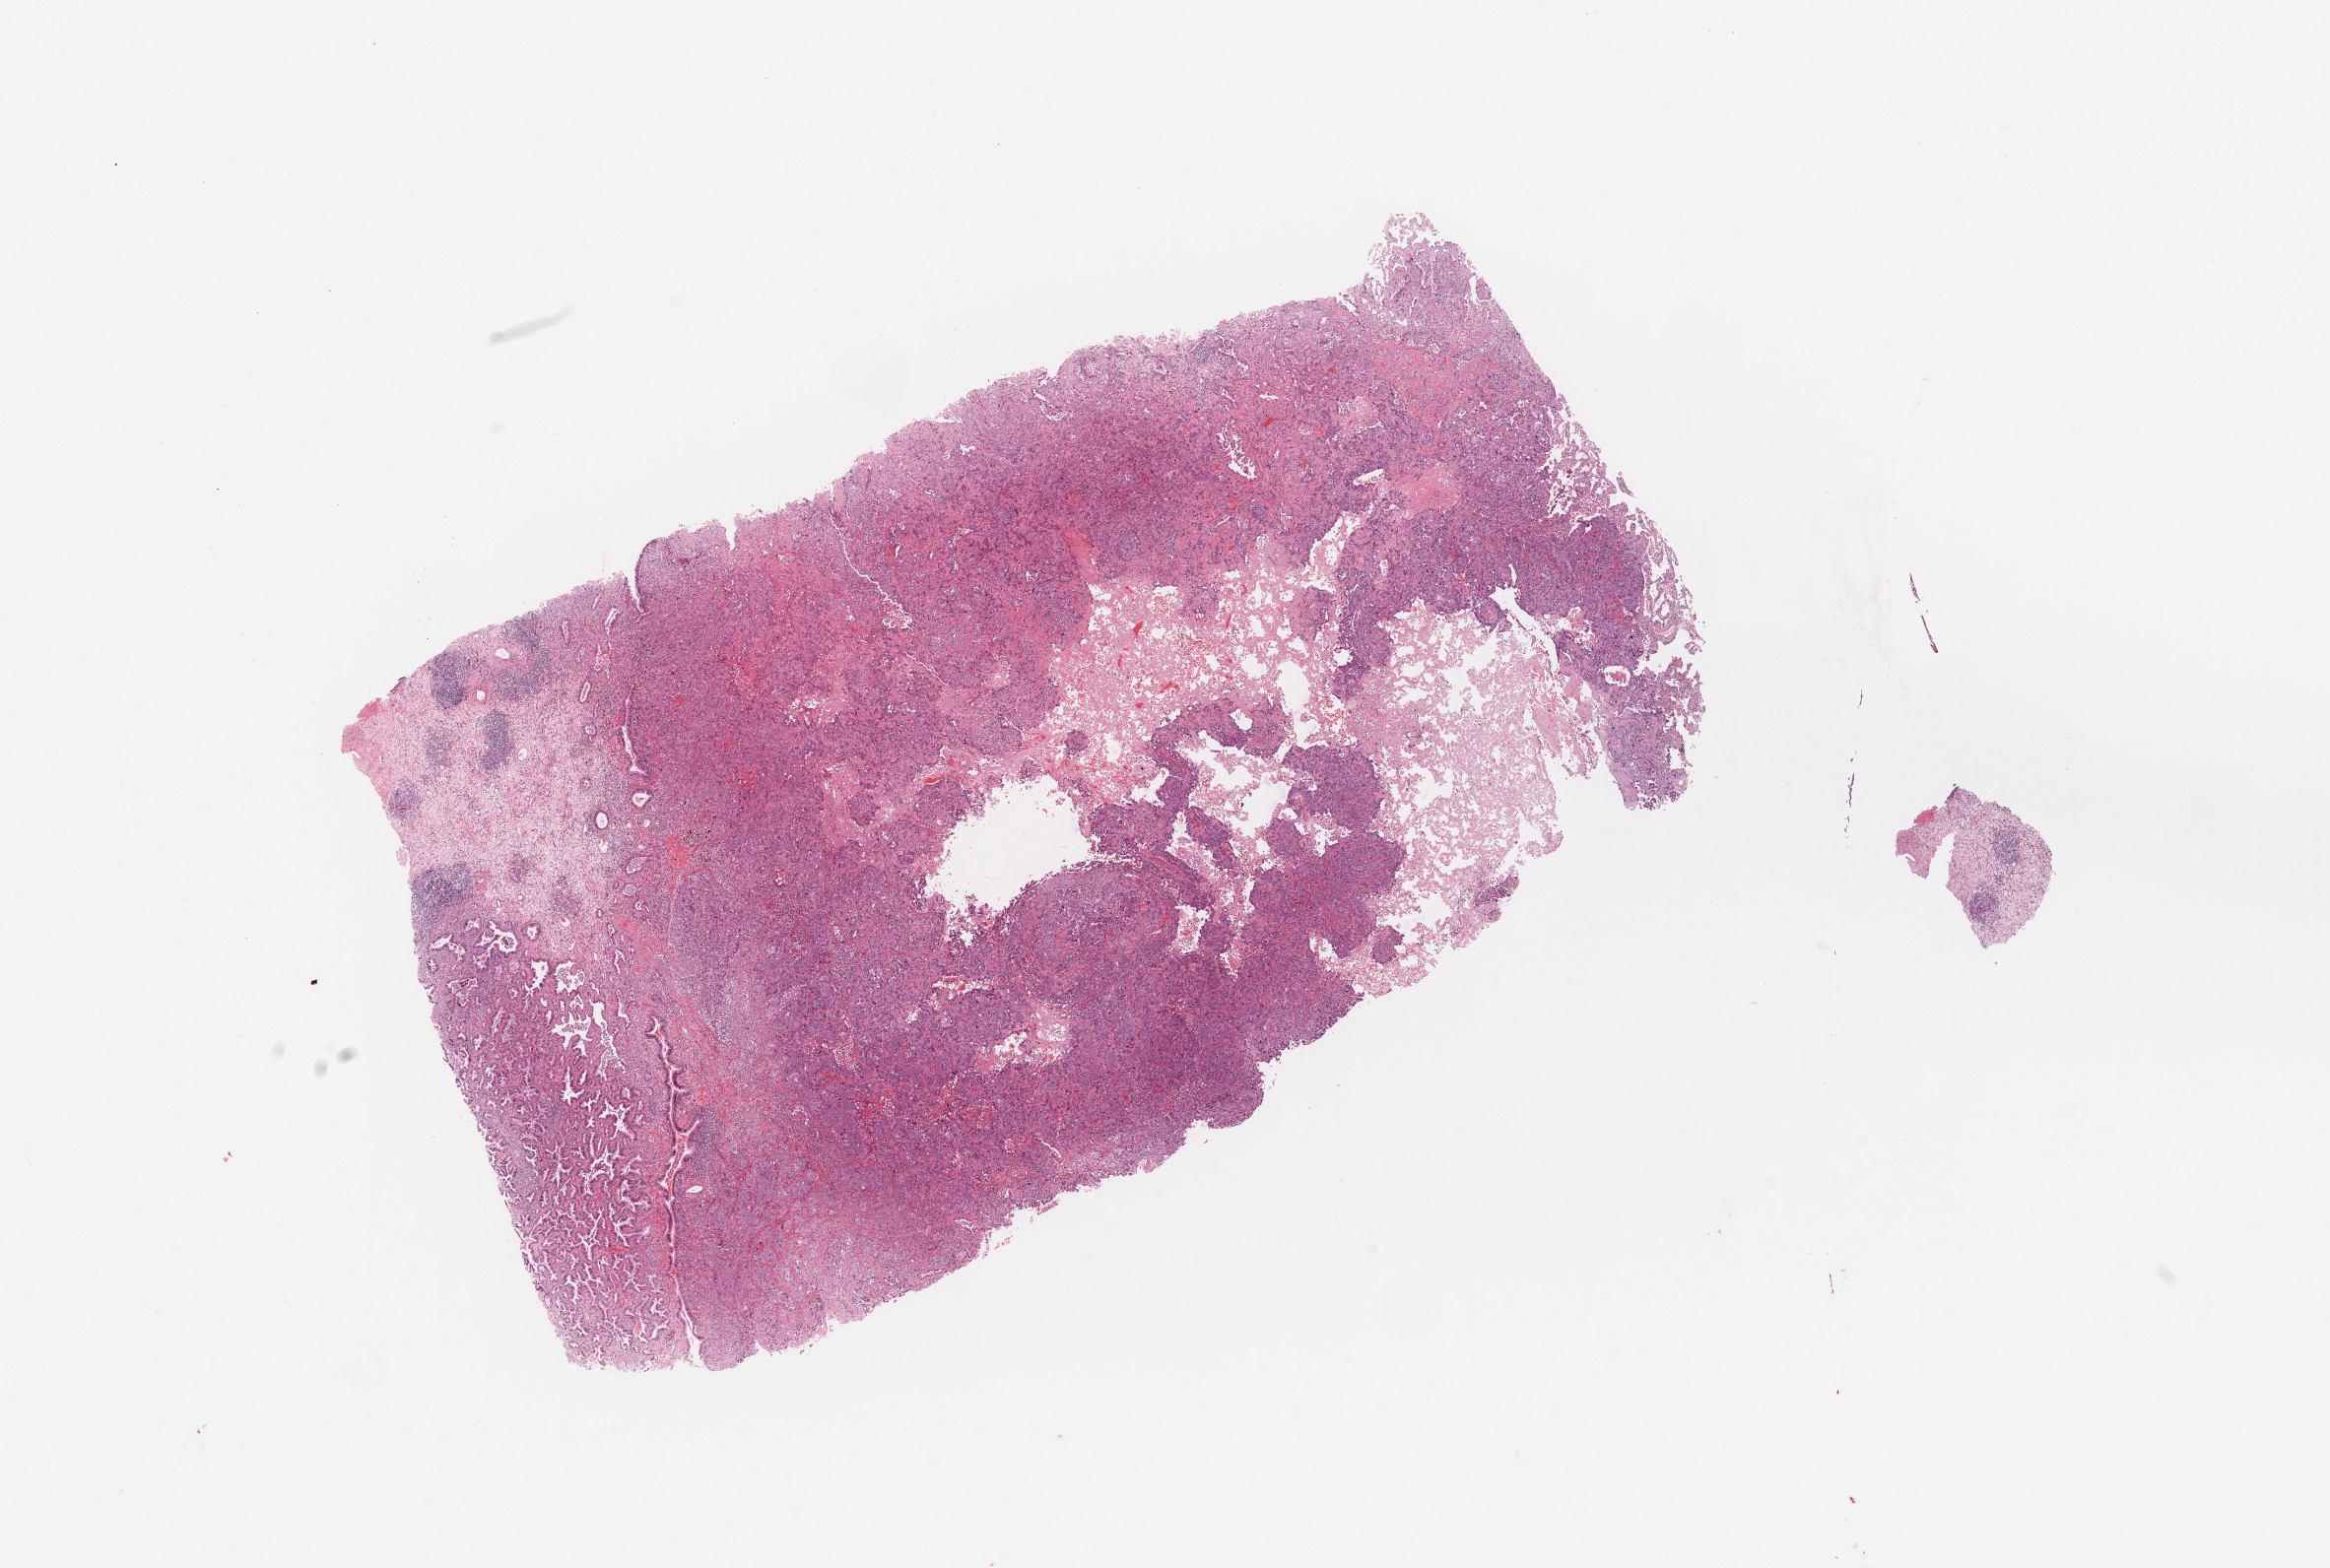
Whole-slide histology image, H&E — low-resolution overview of the scanned area, about 18.7 x 12.6 mm (from a 20x scan). Tumour tissue sample, sampled site: lung. 57-year-old female patient. Histologic grade: G3 (poorly differentiated). Composition of this section per pathologist review: tumour nuclei 70%, necrosis 5%.
Primary tumour site (as recorded): right upper lobe. AJCC pathologic stage: IIA. Diagnosis: Adenocarcinoma, NOS.